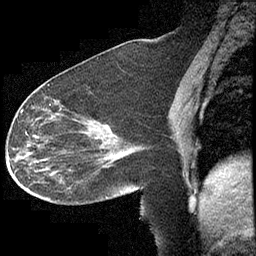
Breast MRI (dynamic contrast-enhanced), one sagittal slice; position 166 of 232 along the scan axis; dynamic contrast-enhanced study with each time point stored as its own series, time point 2 of 4 at this slice position (early post-contrast, ordered by acquisition time); 1.5 T; TE 4.2 ms, TR 6.7 ms; 3 mm slice thickness; 256 × 256 image matrix, field of view 200 × 200 mm. Female patient, age 63 years. Case-level facts recorded for this patient, not image findings: setting: breast cancer imaged before/during neoadjuvant chemotherapy; receptor status: triple-negative.
Outlined on this slice (semi-automatic segmentation, software-assisted and operator-edited):
- analysis volume of interest (the breast-tissue region the enhancement analysis was run in; not a lesion): bounding box <13,90,140,206> (left, top, right, bottom; pixels)
- tumour enhancement mask (voxels above the 70 % enhancement threshold inside the analysis volume of interest): <21,109,43,170>